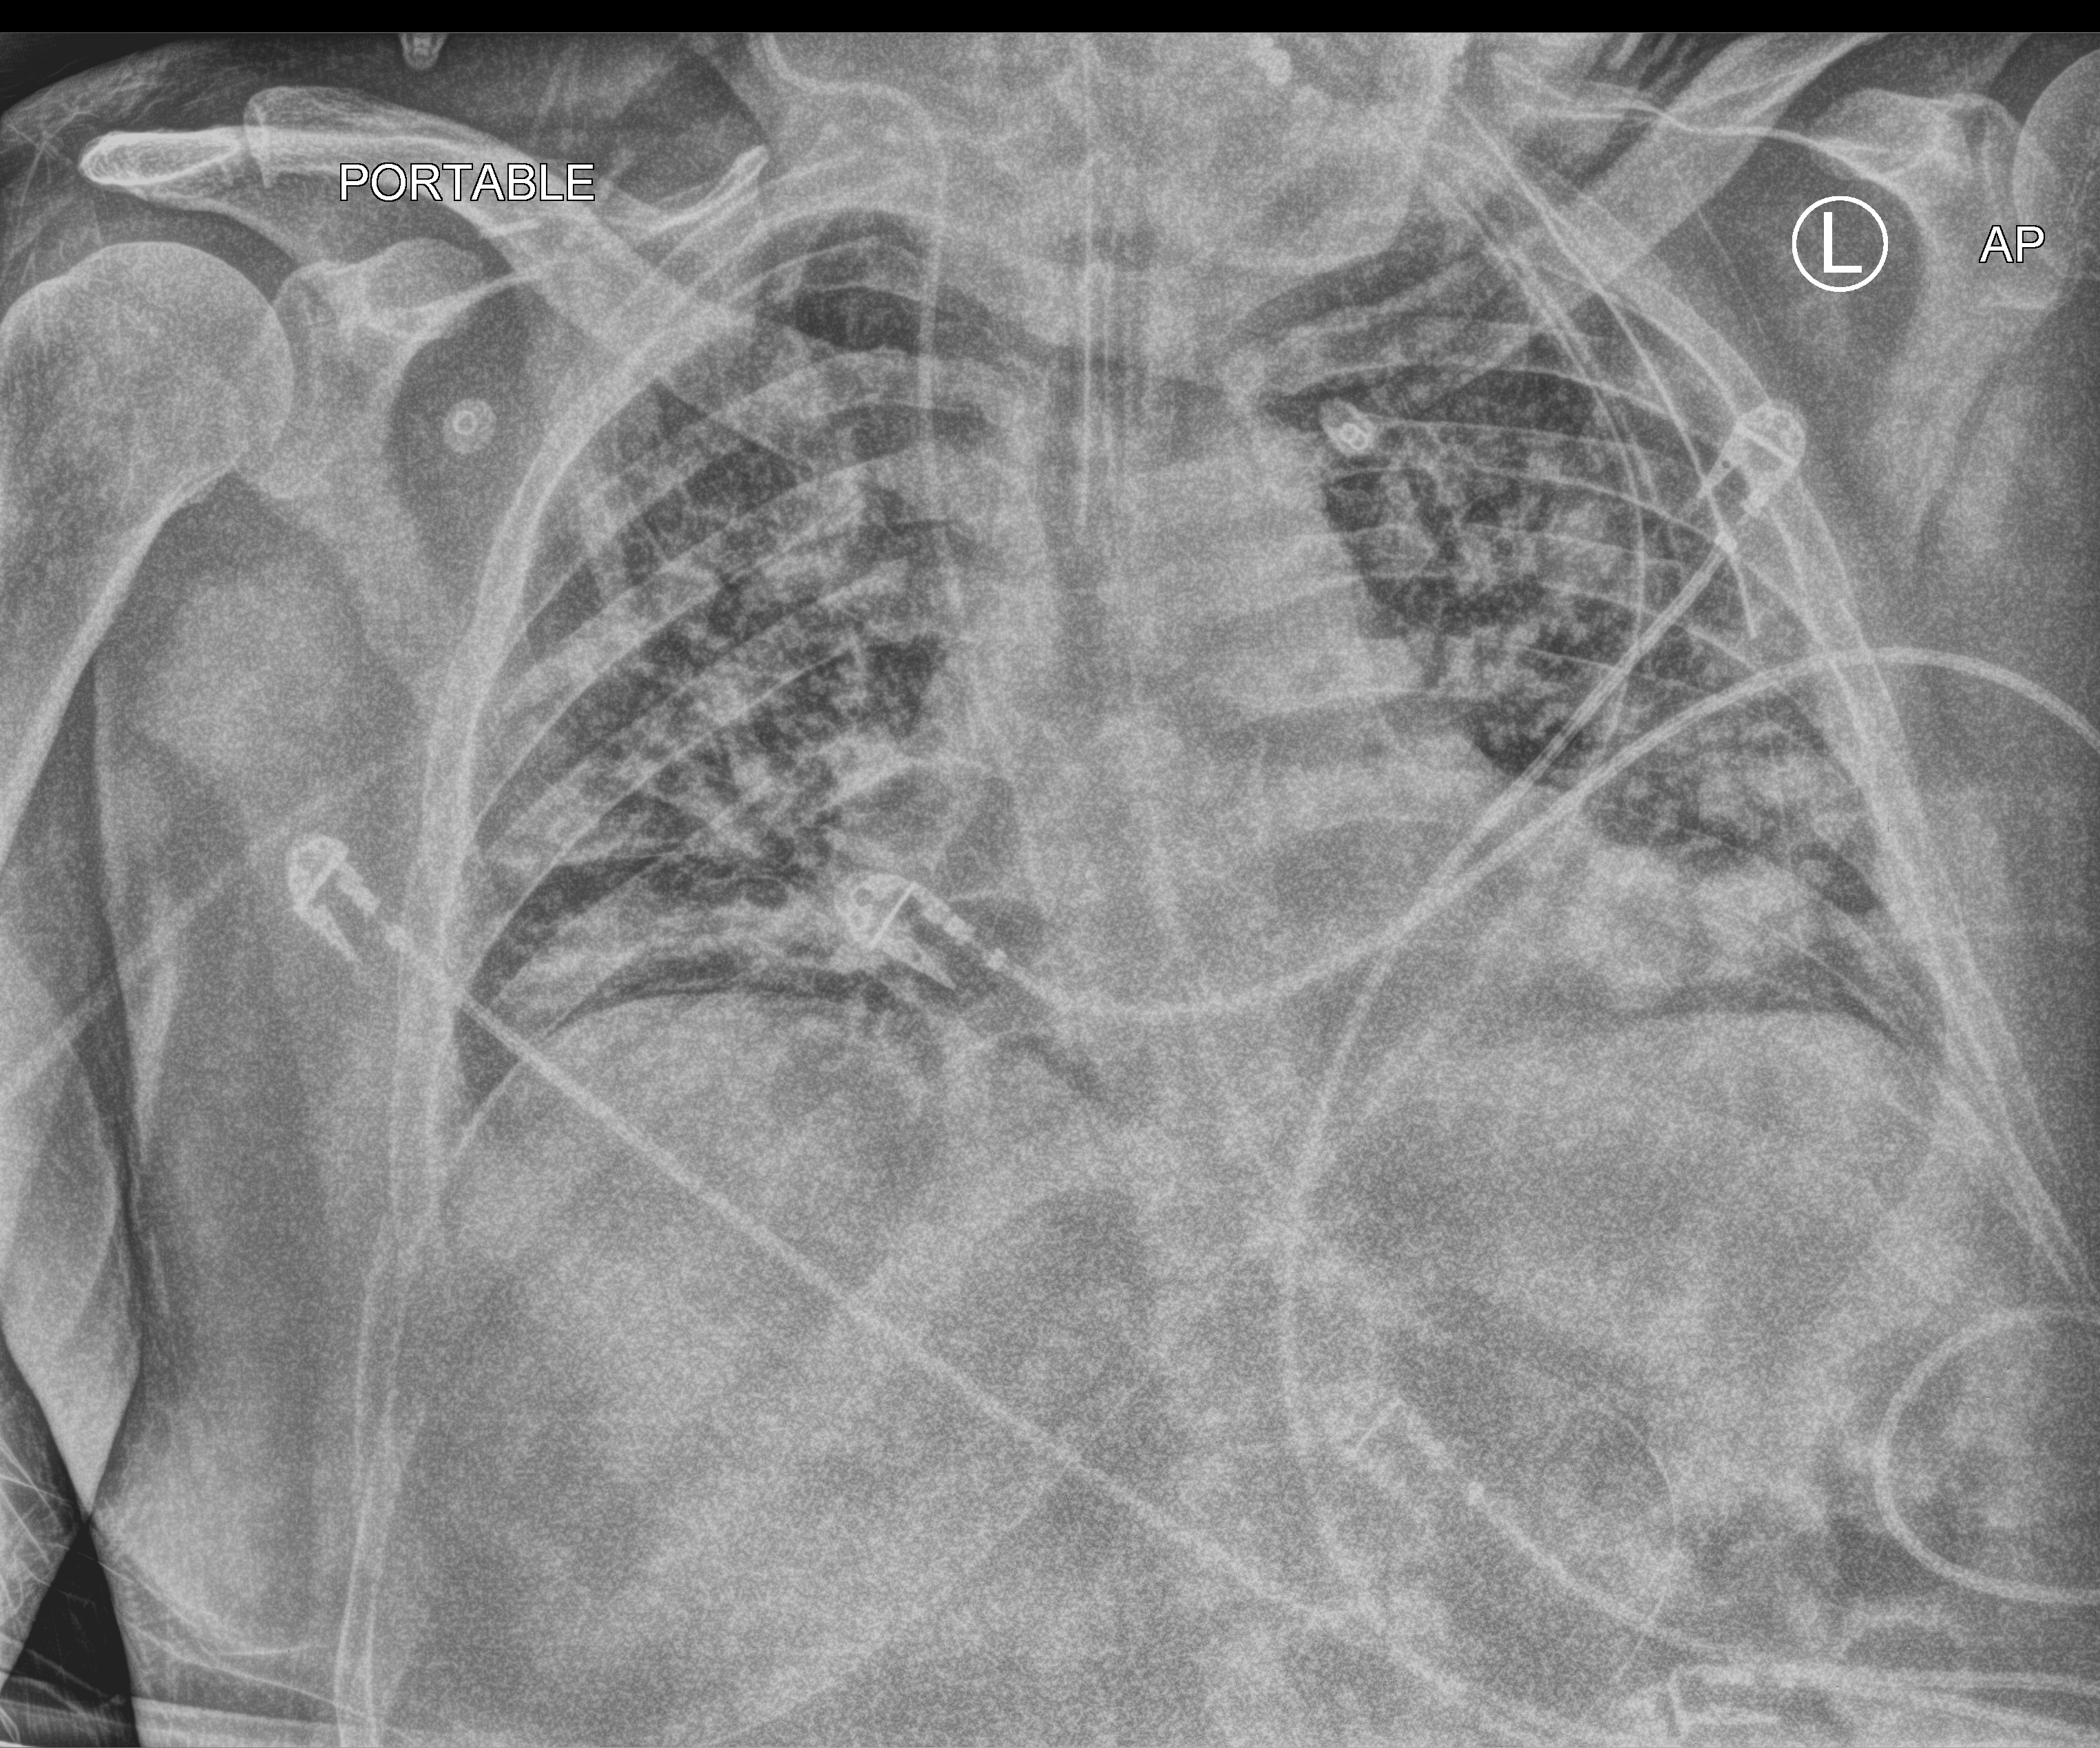
Chest X-ray (portable); anteroposterior (AP) projection. Patient hospitalised with COVID-19; male, aged 18–59 years.
Hospital-stay facts (about this admission, not read from this image; timing relative to this image not recorded): length of hospital stay: 17 days; admitted to intensive care during this hospital stay: yes; COPD (admission record): no.